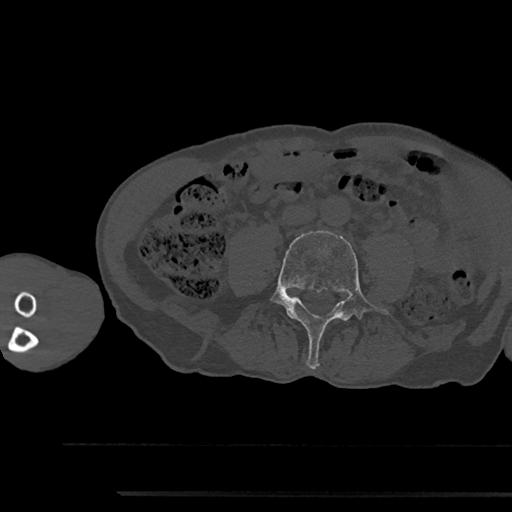
CT including the spine, one axial slice; position 413 of 797 along the scan axis; bone window (W 1800 / L 400 HU); 0.5 mm slice thickness; 512 × 512 image matrix, field of view 367 × 367 mm. Male patient, age 79 years. Case-level facts recorded for this patient, not image findings: primary cancer: prostate.
Structures marked on this image (semi-automatically segmented with operator editing):
- L4 vertebra: bounding box <271,230,391,369> (left, top, right, bottom; pixels)